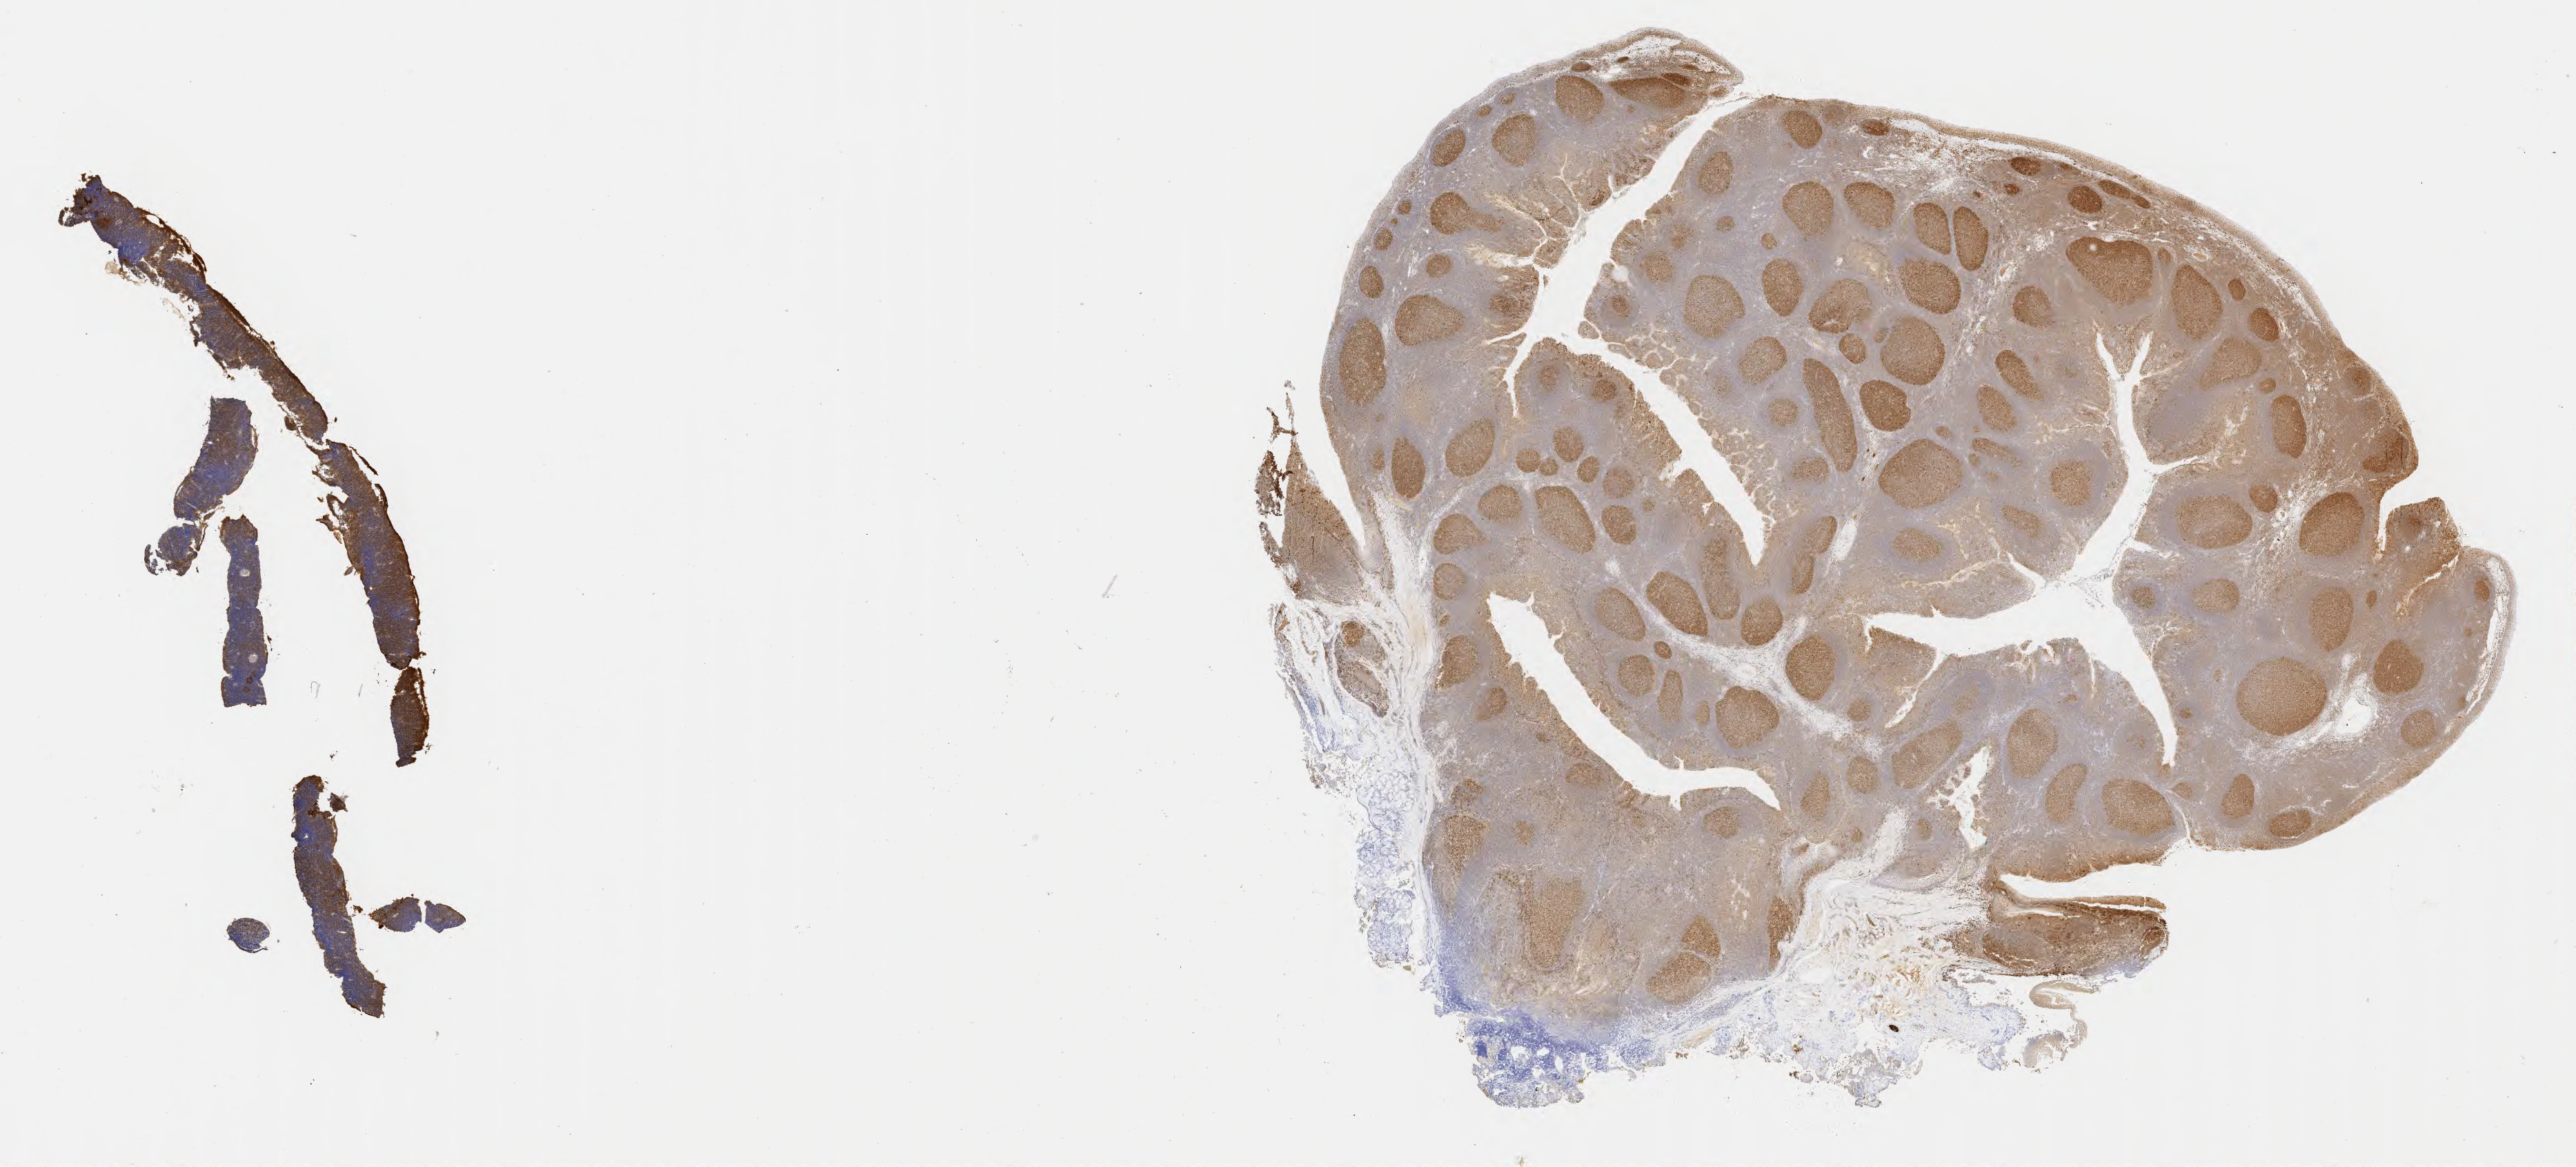
Immunohistochemistry (IHC) whole-slide image stained for BCL6, a low-resolution overview of the entire scanned area, about 30.2 x 13.7 mm; specimen: tumor tissue. Patient: male, age at initial diagnosis 8 years.
Histologic diagnosis: Burkitt lymphoma, NOS.